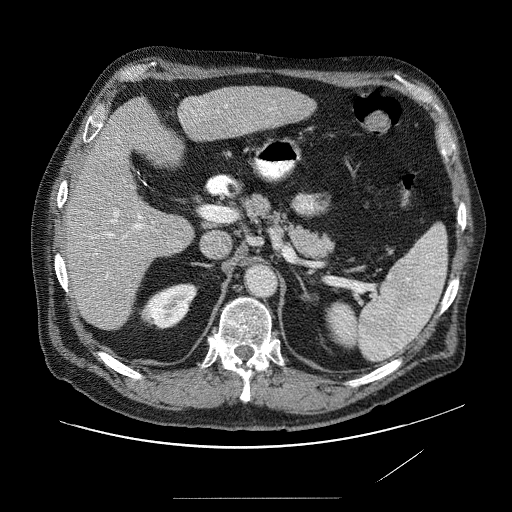
Contrast-enhanced abdominal CT (liver protocol), one axial slice. Position 40 of 89 along the scan axis. Reconstruction kernel STANDARD. 120 kVp. Soft-tissue window (W 400 / L 40 HU). 2.5 mm slice thickness. 512 × 512 image matrix, field of view 420 × 420 mm. From the clinical record (not read from this slice): diagnosis: hepatocellular carcinoma (patient treated with transarterial chemoembolisation; whether this scan precedes or follows treatment is not stated here); TNM stage (as recorded): Stage-IVA; Child-Pugh class: A; tumour differentiation: moderately differentiated; tumour nodularity: multinodular.
Annotated regions visible in this slice (semi-automatically segmented with operator editing):
- liver parenchyma outside the tumour (the mass and vessels are separate outlines, so this box may not span the whole liver): box from (x=60, y=84) to (x=320, y=332) px
- mass: (x=162, y=99)–(x=210, y=255)
- liver vessels: (x=91, y=121)–(x=234, y=293)